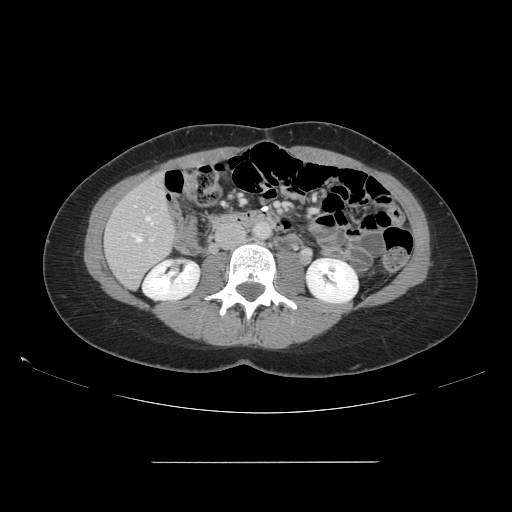
Contrast-enhanced abdominal CT, one axial slice. Slice 47 of 151 in the series (ordered by position). 120 kVp. Intravenous contrast given. Soft-tissue window (W 400 / L 40 HU). 512 × 512 image matrix, field of view 421 × 421 mm. Female patient, age 46 years. Case-level facts recorded for this patient, not image findings: diagnosis: colorectal cancer liver metastases, imaged before liver resection; multiple liver metastases: yes; largest metastasis: 3 cm; disease in both lobes: yes.
Structures marked on this image (expert manual segmentation):
- hepatic veins: box from (x=136, y=217) to (x=151, y=242) px
- liver: (x=105, y=175)–(x=175, y=288)
- planned liver remnant (the part of the liver to remain after resection): (x=105, y=175)–(x=175, y=288)